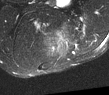
MRI of an extremity soft-tissue mass, one axial slice. Position 40 of 52 along the scan axis. T2-weighted fat-saturated. MR volume resampled by the dataset authors to the PET/CT grid (not the native acquisition matrix). 109 × 95 image matrix. Male patient. From the clinical record (not read from this slice): histological type: synovial sarcoma; site of the primary tumour: left poplietal fossa.
Structures marked on this image (expert contour drawn on MRI and transferred to this co-registered scan by the dataset authors):
- gross tumour volume (mass): bounding box (x1, y1, x2, y2) in pixels: (42, 36, 52, 52)